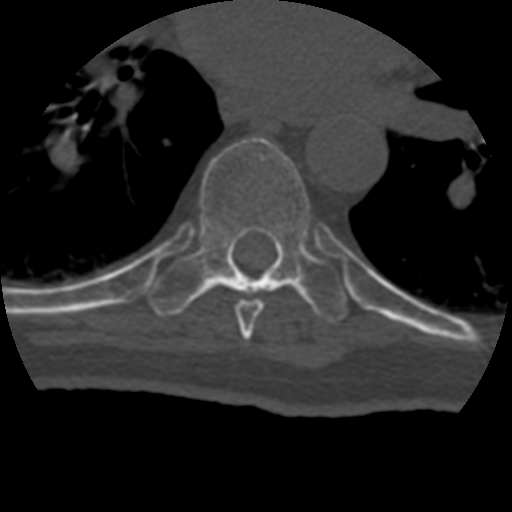
CT including the spine, one axial slice; slice 267 of 399 in the series (ordered by position); 120 kVp; bone window (W 1800 / L 400 HU); 512 × 512 image matrix, field of view 160 × 160 mm. Patient age 69 years. Case-level facts recorded for this patient, not image findings: primary cancer: prostate.
Structures marked on this image (semi-automatically segmented with operator editing):
- T7 vertebra: bounding box [x1, y1, x2, y2] px = [235, 299, 264, 339]
- T8 vertebra: [146, 137, 348, 322]